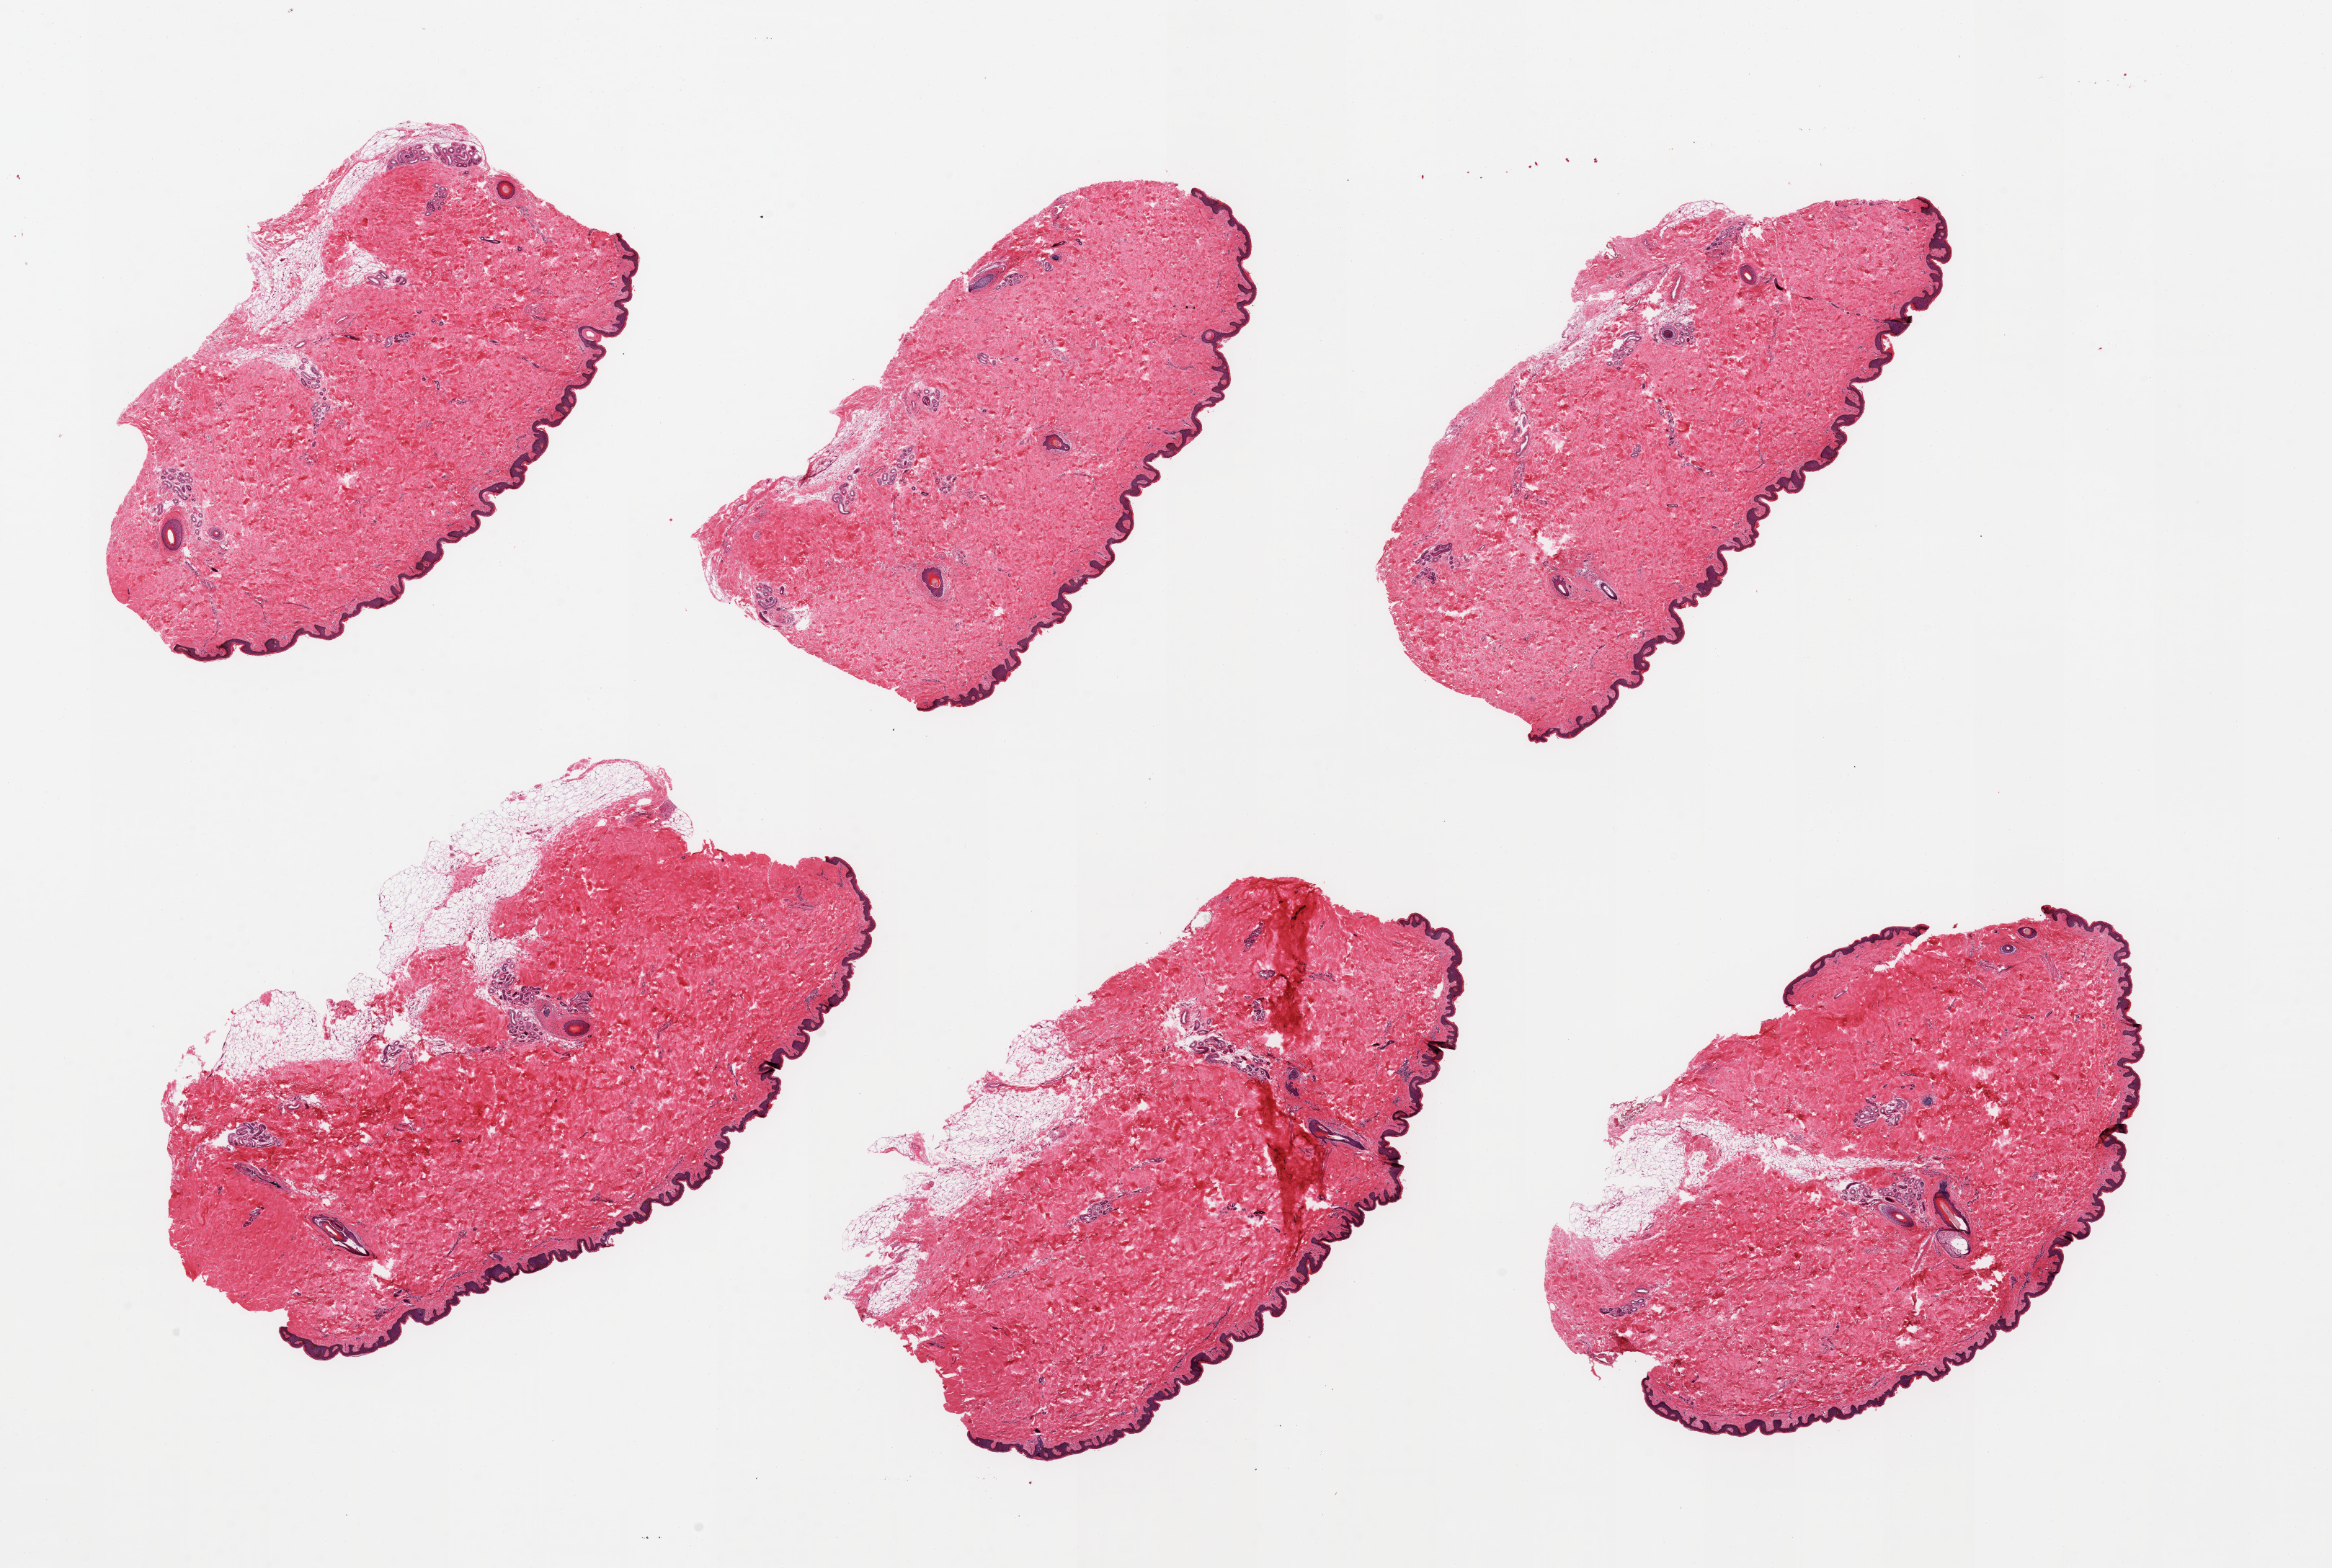
Whole-slide image, haematoxylin and eosin stain, brightfield — shown as a low-resolution overview of the whole scanned area (about 25.6 x 17.2 mm, slide scanned at 20x). PAXgene-fixed paraffin-embedded (PFPE) section. Target tissue: skin of suprapubic region. Donor tissue sample.
Review note (as recorded): 6 pieces, adherent dermal fat ,~0.7mm; squamous epithelium is ~40-50 microns.